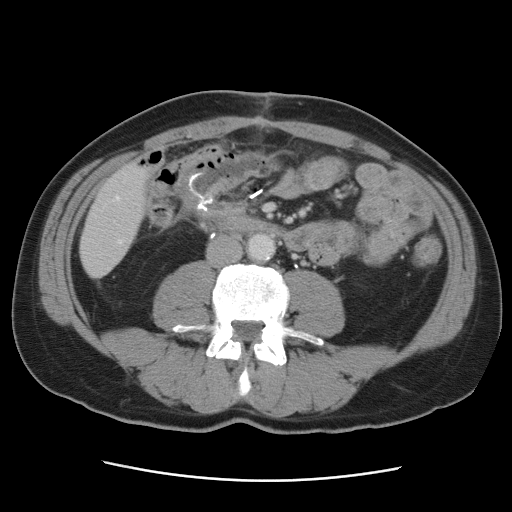
Contrast-enhanced abdominal CT, one axial slice; position 14 of 89 along the scan axis; 120 kVp; intravenous contrast given; soft-tissue window (W 400 / L 40 HU); 5 mm slice thickness; 512 × 512 image matrix, field of view 366 × 366 mm. Male patient, age 59 years. Case-level facts recorded for this patient, not image findings: diagnosis: colorectal cancer liver metastases, imaged before liver resection; multiple liver metastases: yes; largest metastasis: 0.6 cm.
Structures marked on this image (expert manual segmentation):
- hepatic veins: bounding box [x1, y1, x2, y2] px = [115, 196, 122, 243]
- liver: [81, 164, 149, 277]
- planned liver remnant (the part of the liver to remain after resection): [81, 164, 148, 258]